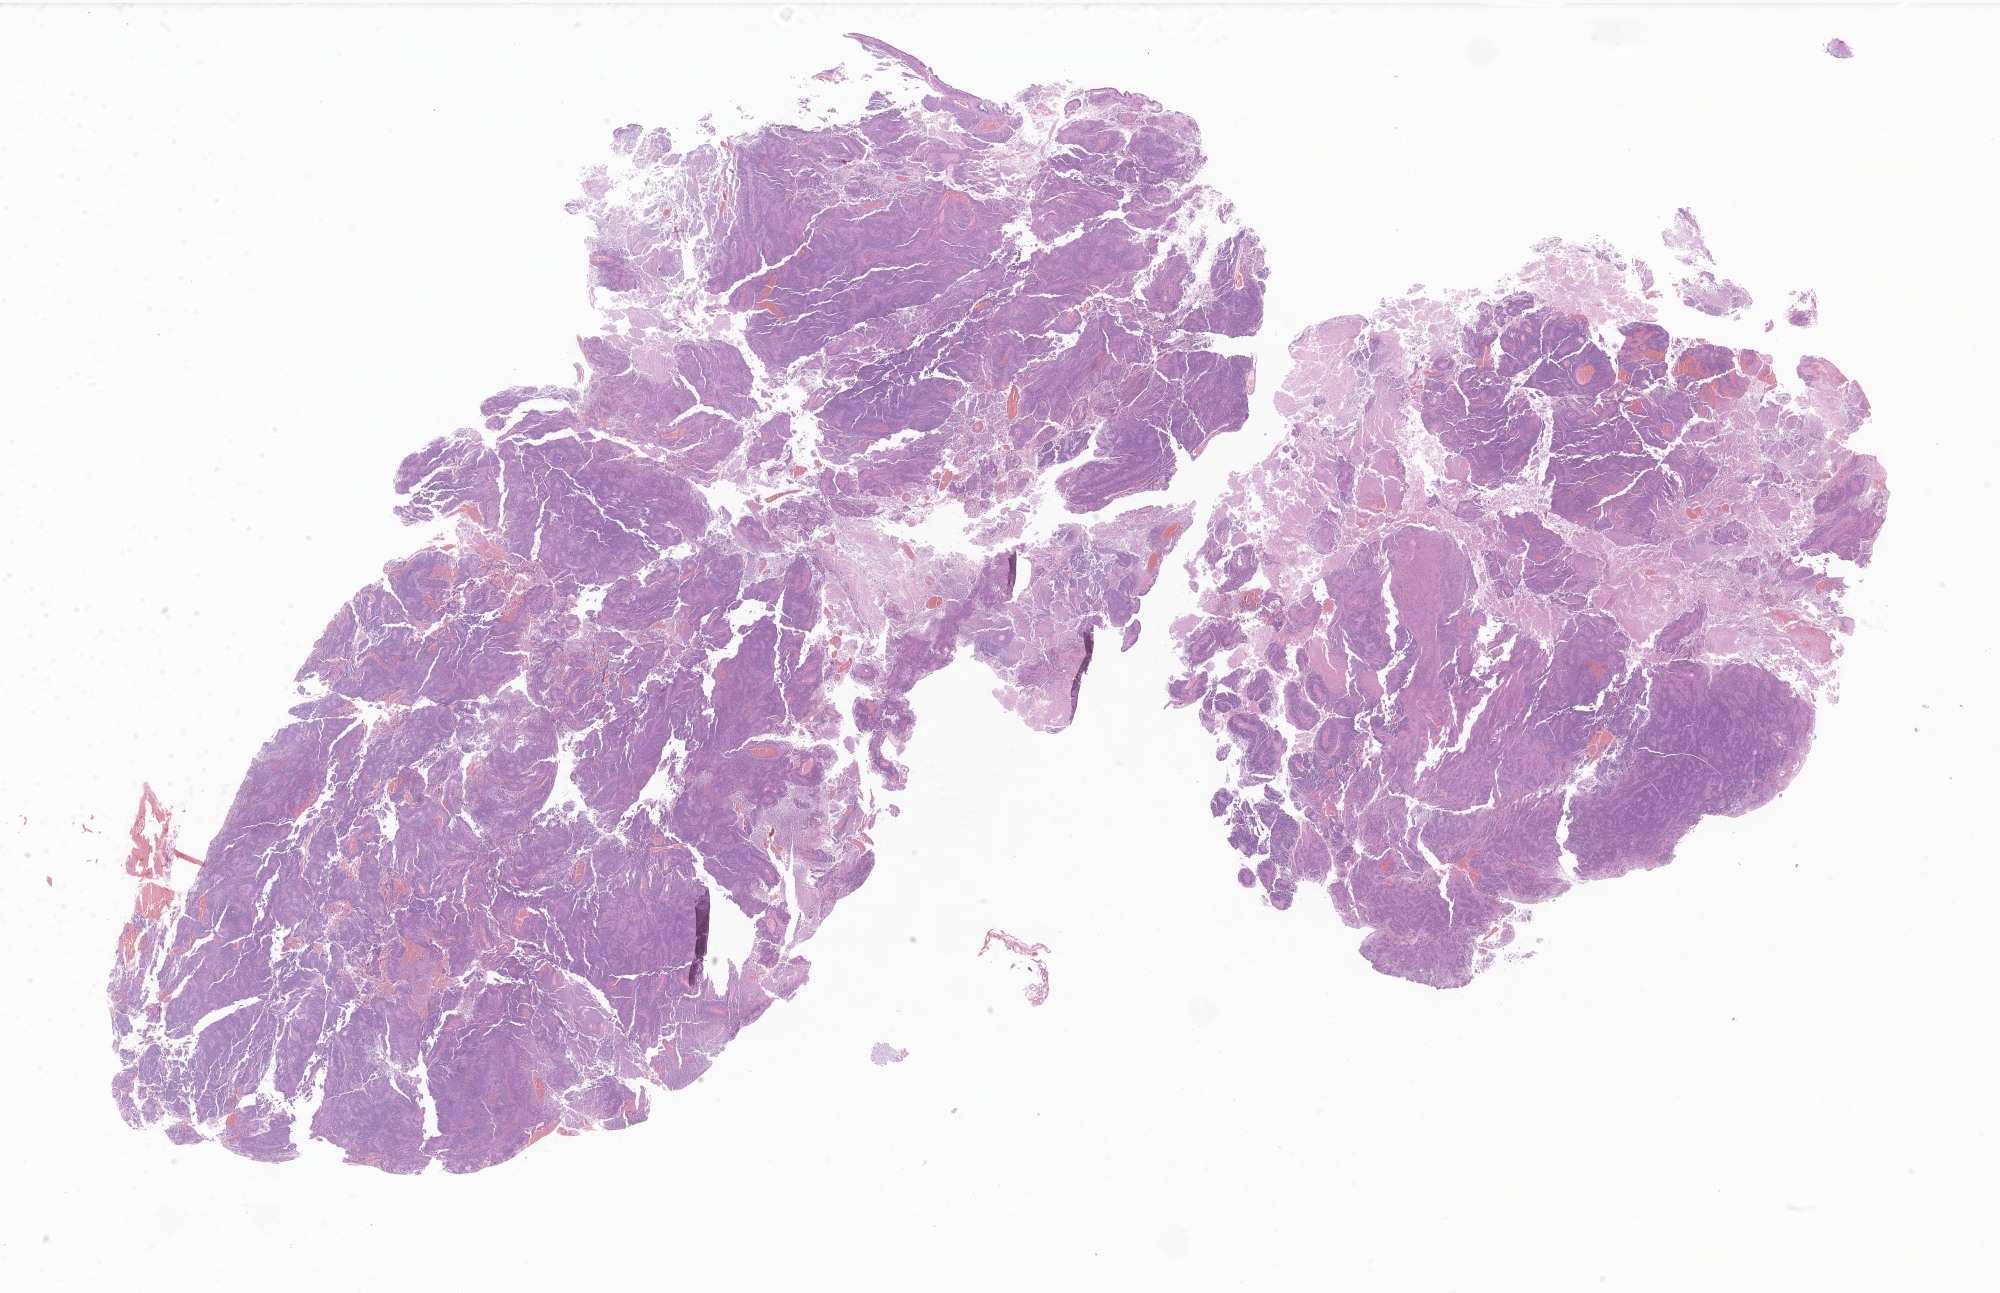
Whole-slide image, haematoxylin and eosin stain of tumor tissue from the brain, shown as a low-resolution overview of the whole scanned area (about 33.7 x 21.8 mm), FFPE section. Patient male; age 199 months (16 years 7 months).
Diagnosis: Ependymoma, anaplastic.